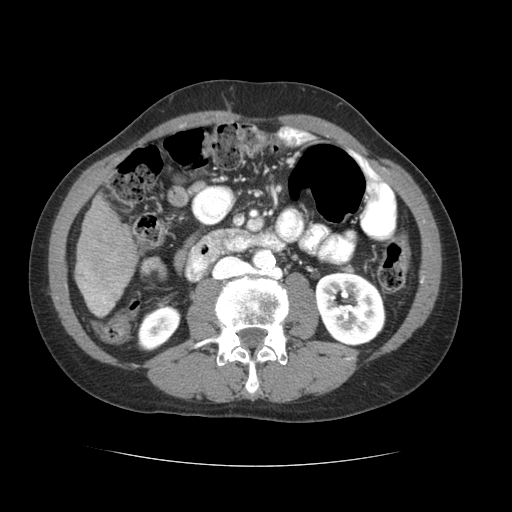
Contrast-enhanced abdominal CT (liver protocol), one axial slice; slice 14 of 69 in the series (ordered by position); reconstruction kernel STANDARD; soft-tissue window (W 400 / L 40 HU); 2.5 mm slice thickness; 512 × 512 image matrix, field of view 360 × 360 mm. Case-level facts recorded for this patient, not image findings: diagnosis: hepatocellular carcinoma (patient treated with transarterial chemoembolisation; whether this scan precedes or follows treatment is not stated here); TNM stage (as recorded): Stage-II; Child-Pugh class: B; tumour differentiation: poorly differentiated; tumour nodularity: multinodular.
Structures marked on this image (semi-automatically segmented with operator editing):
- liver parenchyma outside the tumour (the mass and vessels are separate outlines, so this box may not span the whole liver): bounding box <74,196,138,316> (left, top, right, bottom; pixels)
- liver vessels: <84,272,113,314>